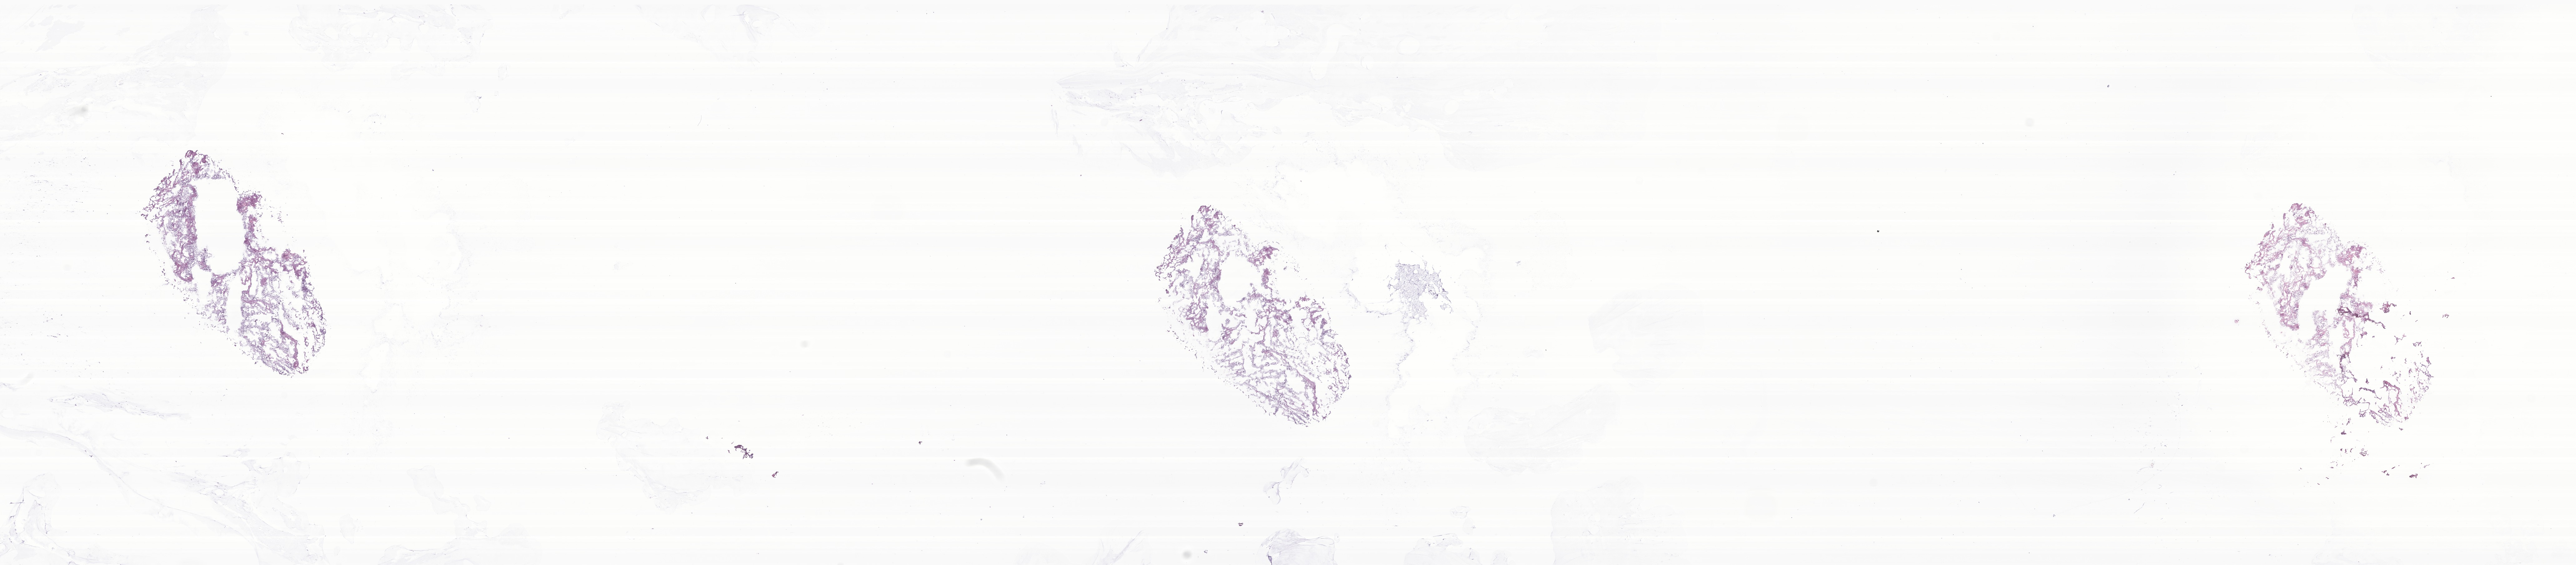
Haematoxylin and eosin whole-slide image of tumor tissue from the cerebellum, a low-resolution overview of the entire scanned area, about 34.8 x 7.6 mm; cryosection (OCT / tissue freezing medium). Male patient, age 927 days.
* diagnosis (ICD-O-3 morphology term): Pilocytic astrocytoma